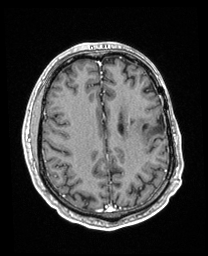
Brain MRI from a brain-tumour surgery series, one axial slice. Position 81 of 208 along the scan axis. T1-weighted post-contrast. 1 mm slice thickness. 208 × 256 image matrix, field of view 211 × 260 mm. Case-level facts recorded for this patient, not image findings: histopathology: Astrocytoma; WHO grade: 3; IDH mutation: yes; tumour location: Left Insular.
Structures marked on this image (outlined manually by an expert reader):
- previous resection cavity: bounding box <143,115,165,133> (left, top, right, bottom; pixels)